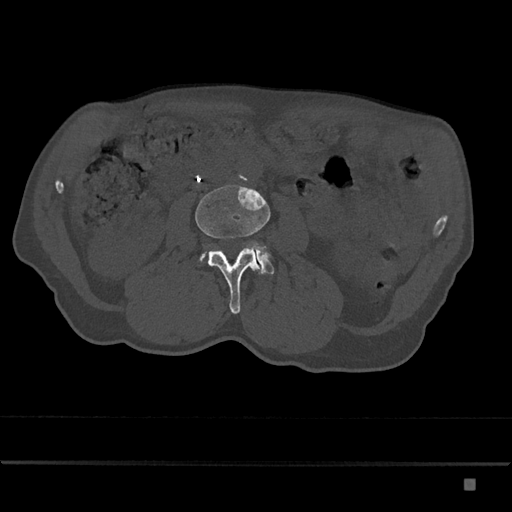
CT including the spine, one axial slice. Slice 391 of 797 in the series (ordered by position). Reconstruction kernel Br40s/3. Bone window (W 1800 / L 400 HU). 0.5 mm slice thickness. 512 × 512 image matrix, field of view 390 × 390 mm. Patient: male, 72 years. From the clinical record (not read from this slice): primary cancer: prostate.
Annotated regions visible in this slice (semi-automatic segmentation, software-assisted and operator-edited):
- L3 vertebra: box from (x=195, y=185) to (x=271, y=314) px
- L4 vertebra: (x=199, y=244)–(x=274, y=274)